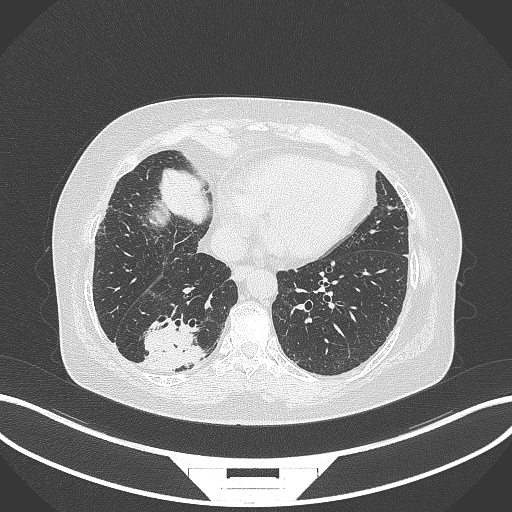
Chest CT, one axial slice; reconstruction kernel B70f; 120 kVp; lung window (W 1500 / L -600 HU); 1 mm slice thickness; 512 × 512 image matrix, field of view 400 × 400 mm. Patient: female, 65 years. Case-level facts recorded for this patient, not image findings: clinical TNM (as recorded): T2b N1 M0; histopathological grade: G1.
Annotated regions visible in this slice (rectangle marked by the reading radiologist):
- lung tumour (recorded histology: adenocarcinoma): box from (x=137, y=314) to (x=210, y=373) px